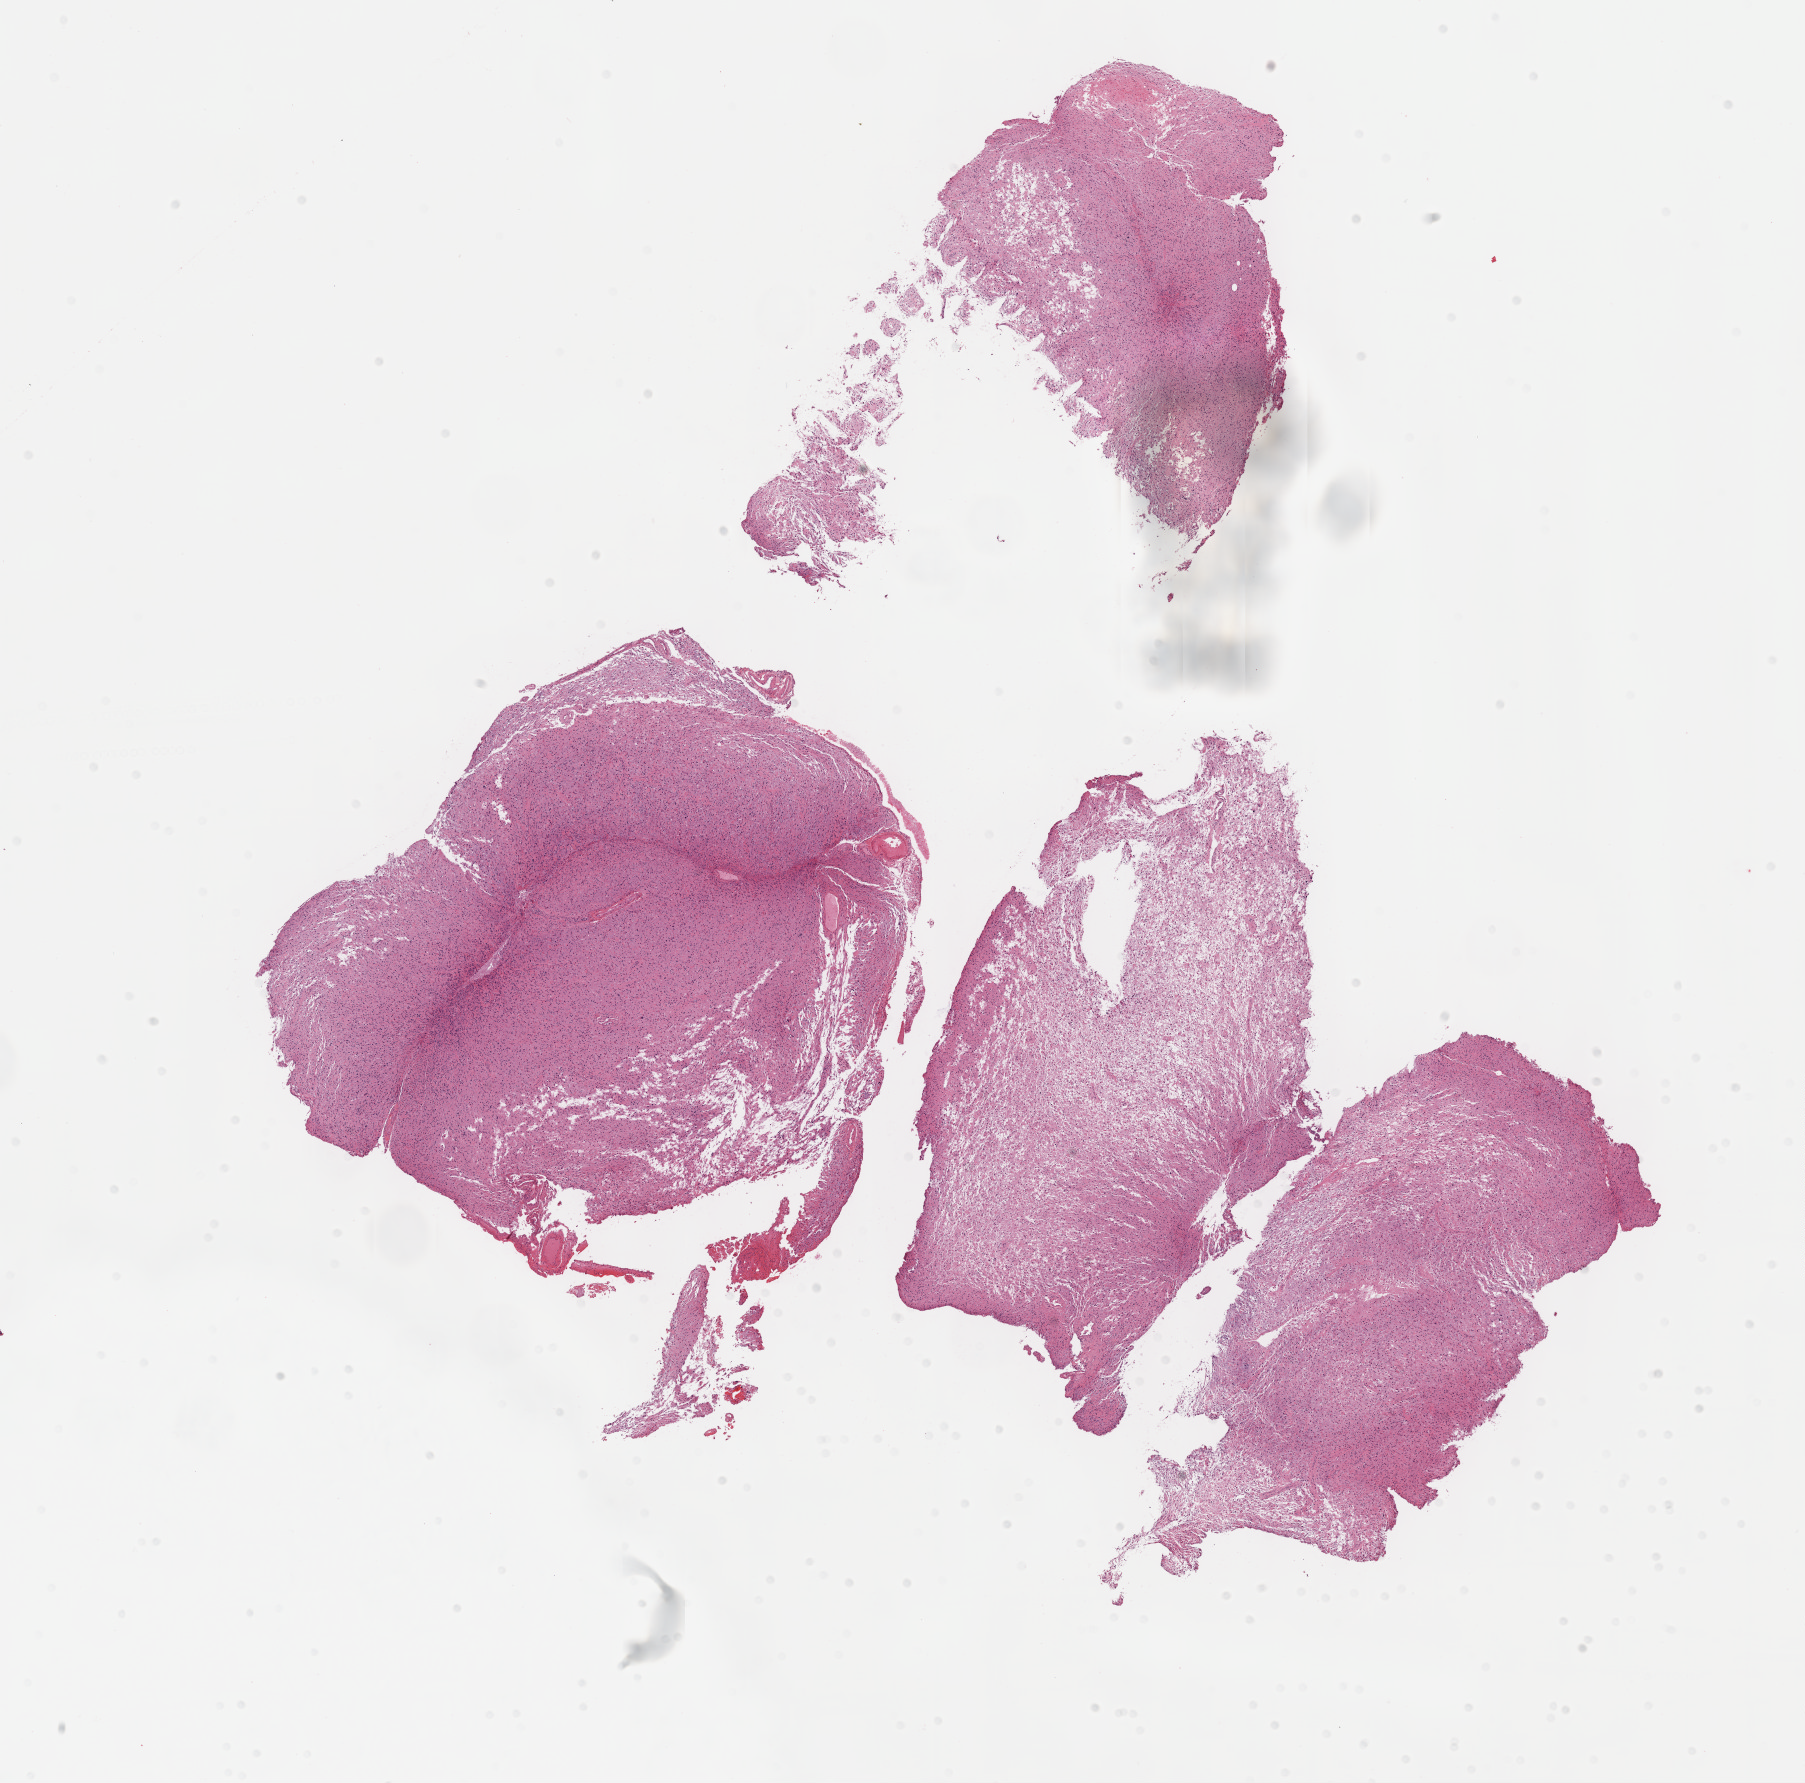
Whole-slide histology image, Hematoxylin and eosin (H&E) stained — low-resolution overview of the scanned area, about 14.6 x 14.4 mm; formalin-fixed paraffin-embedded (FFPE) diagnostic section; brain, primary tumour sample. Female, age 29 years at initial diagnosis. Histologic grade: G3 (poorly differentiated).
Pathologic diagnosis: Astrocytoma, anaplastic (cerebrum).